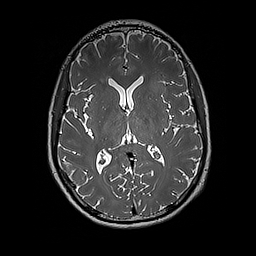
Brain MRI from a brain-tumour surgery series, one axial slice. Position 95 of 192 along the scan axis. 256 × 256 image matrix, field of view 250 × 250 mm. Case-level facts recorded for this patient, not image findings: histopathology: Glioblastoma; WHO grade: 4.
Structures marked on this image (expert manual segmentation):
- tumour: bounding box <152,76,165,95> (left, top, right, bottom; pixels)